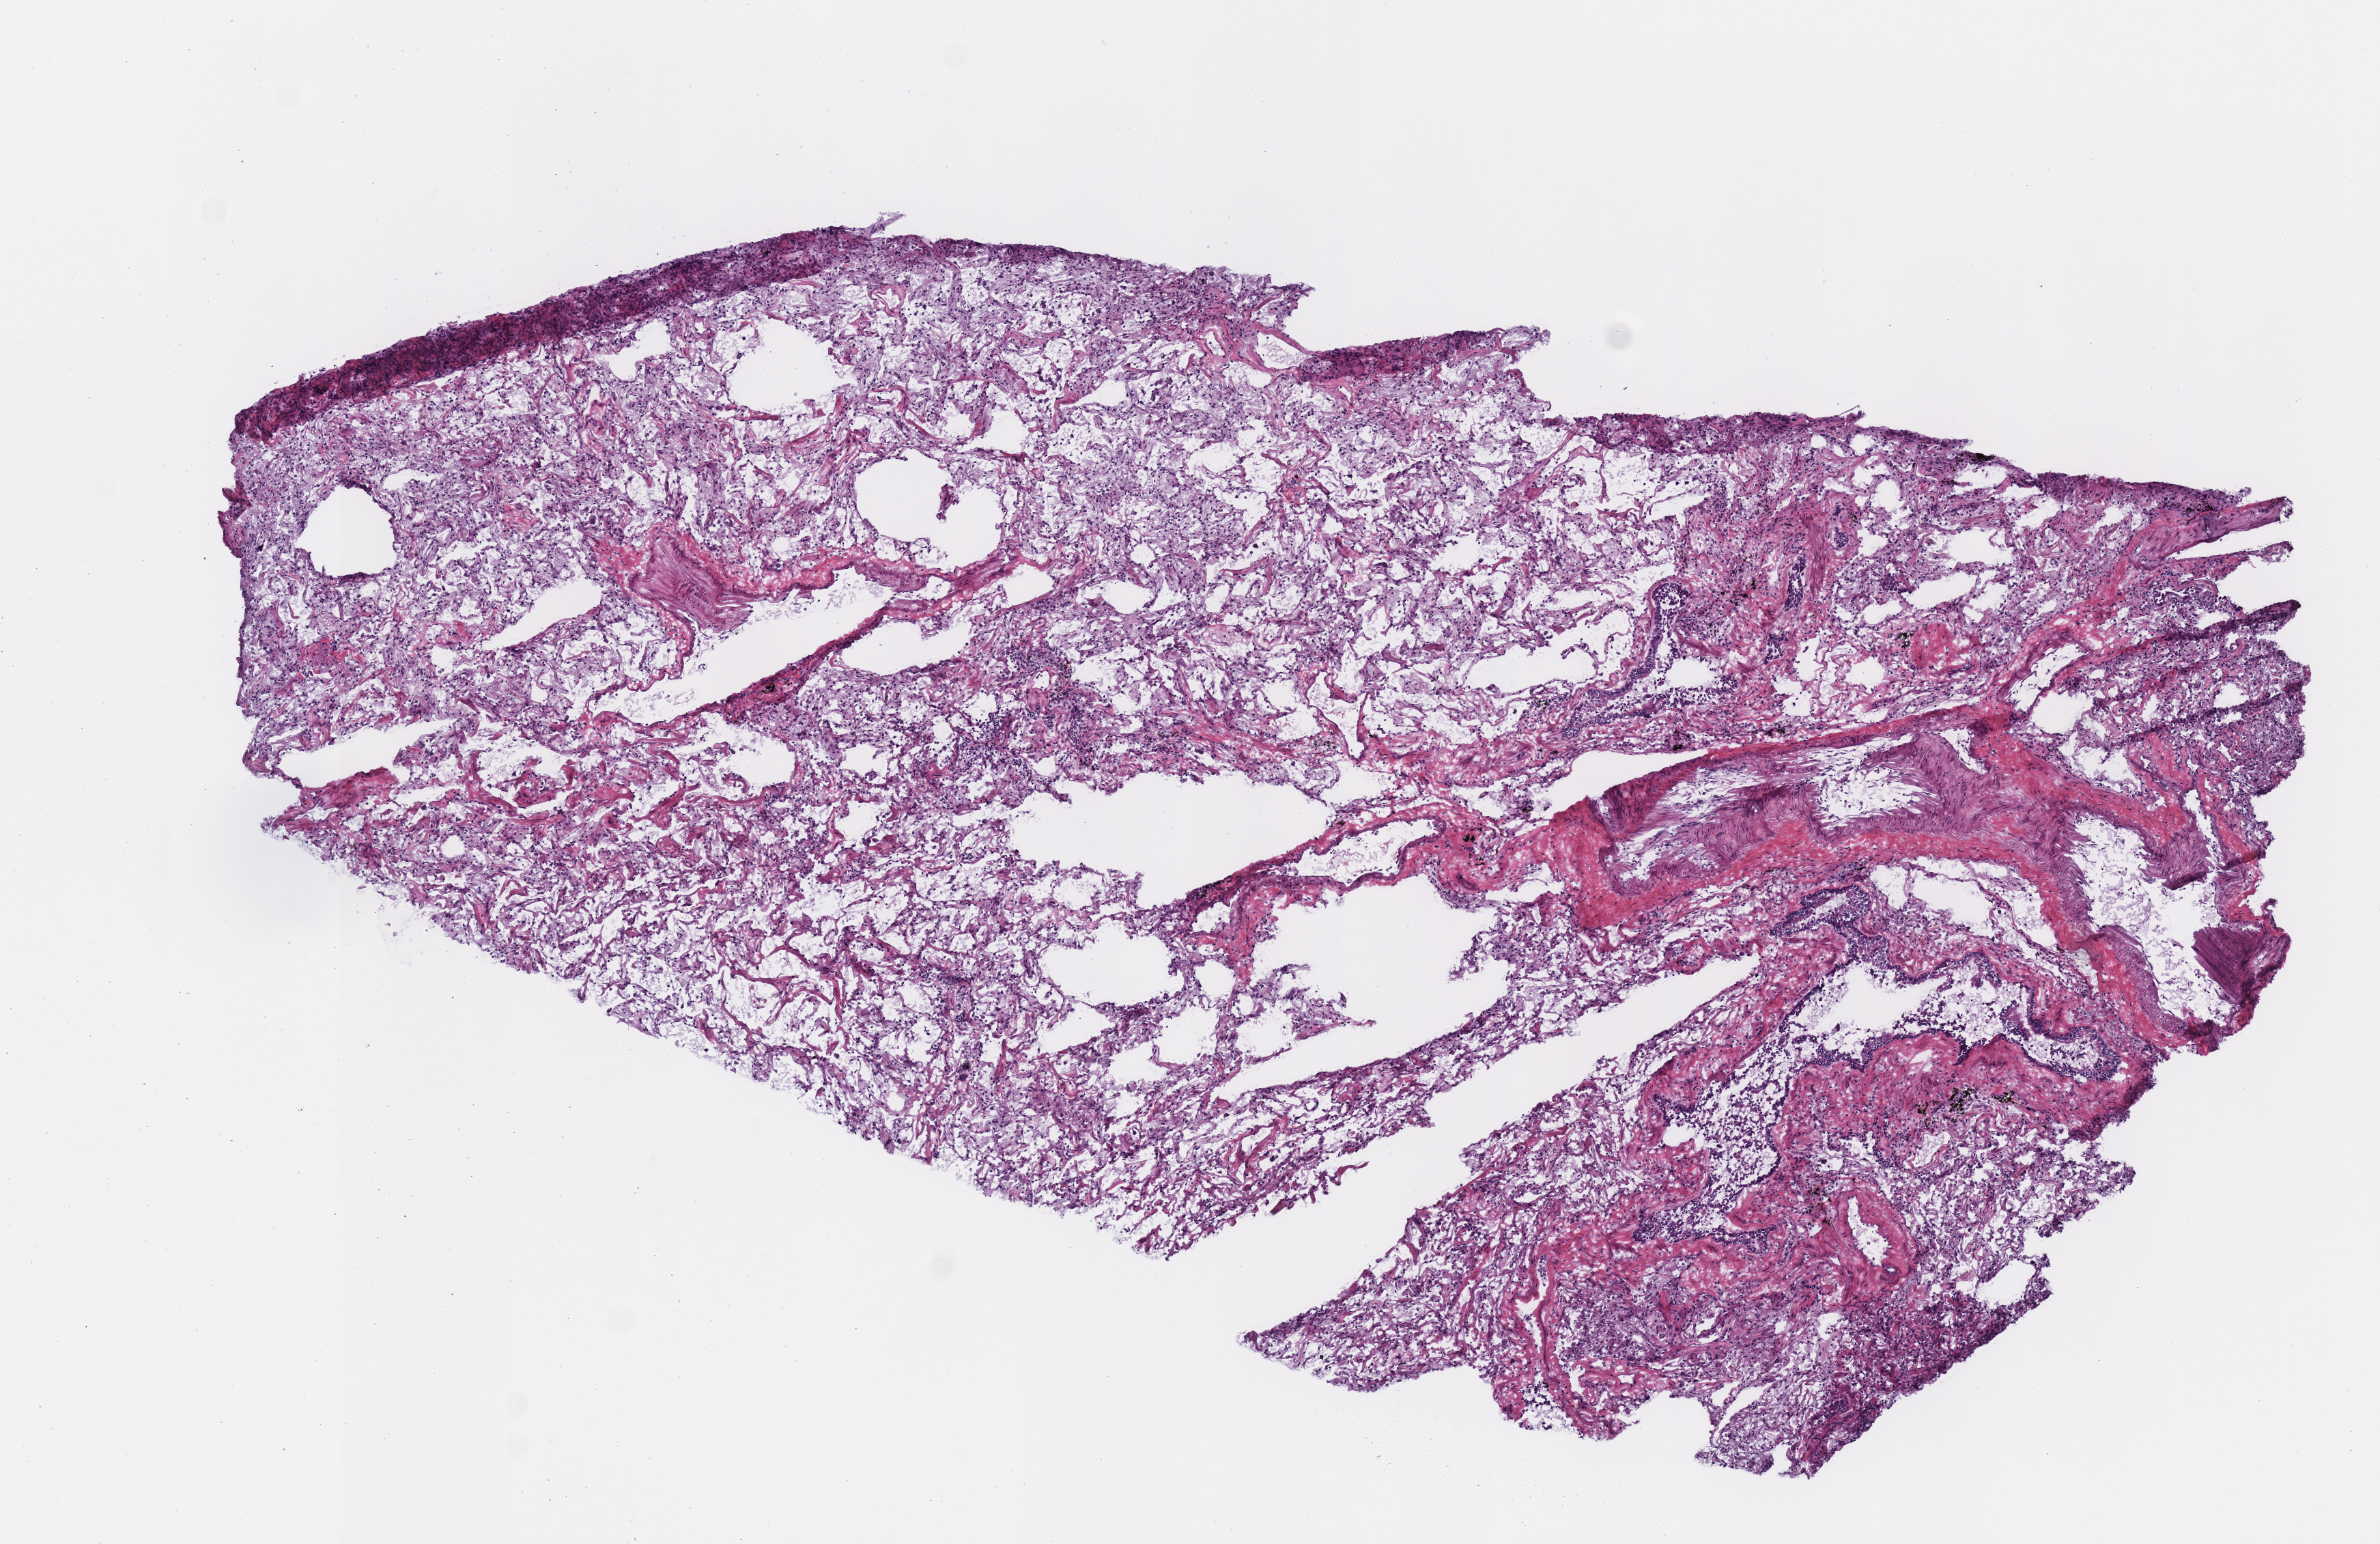
Digitized Hematoxylin and eosin (H&E) stained tissue section (whole slide) — shown as a low-resolution overview of the whole scanned area (about 6.9 x 4.4 mm); frozen section from the top of the tissue portion; solid tissue normal (non-tumour tissue) sample from the lung. Female, age 58 years at initial diagnosis.
This section: solid tissue normal (non-tumour) sample from the same patient. Patient diagnosis: Adenocarcinoma, NOS (upper lobe, lung).